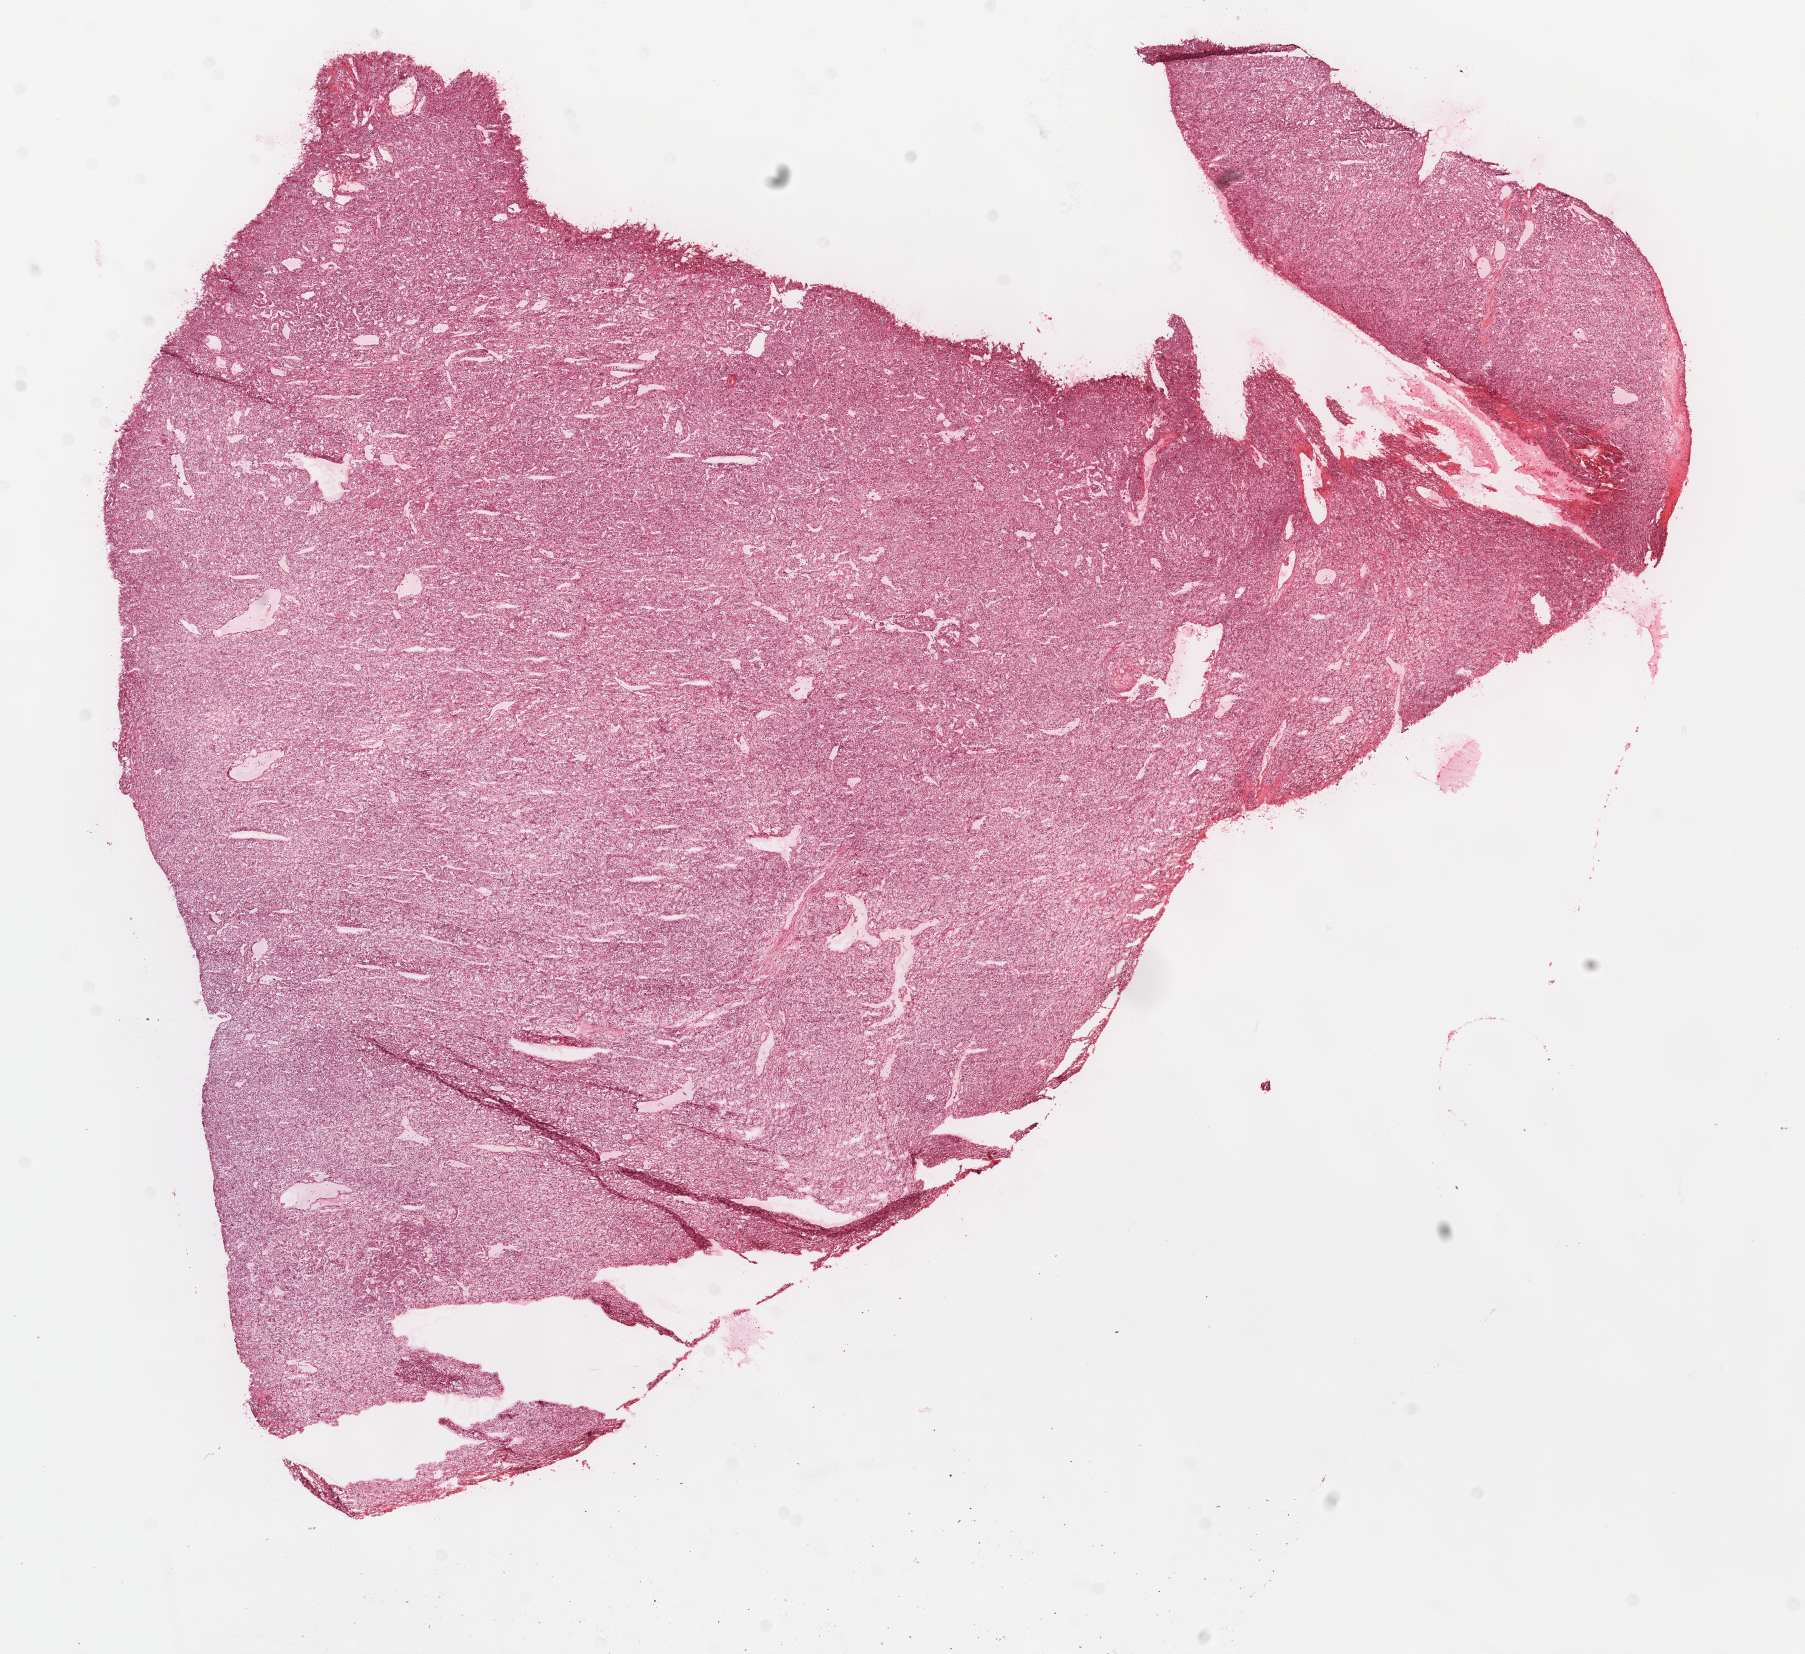
Digitized Hematoxylin and eosin (H&E) stained tissue section (whole slide), whole scanned area (about 14.6 x 13.4 mm, from a 40x scan) shown as a low-resolution overview; frozen section from the top of the tissue portion; kidney, primary tumour sample. Male, age 81 years at initial diagnosis. Histologic grade: G3 (poorly differentiated). Slide review estimates, as recorded: tumour cells 95%, tumour nuclei 85%, normal cells 0%, stromal cells 5%, necrosis 0%.
Diagnosis: Clear cell adenocarcinoma, NOS. Lymph nodes positive (case pathology): 0 of 1 examined. Laterality: right. AJCC pathologic stage: IV.